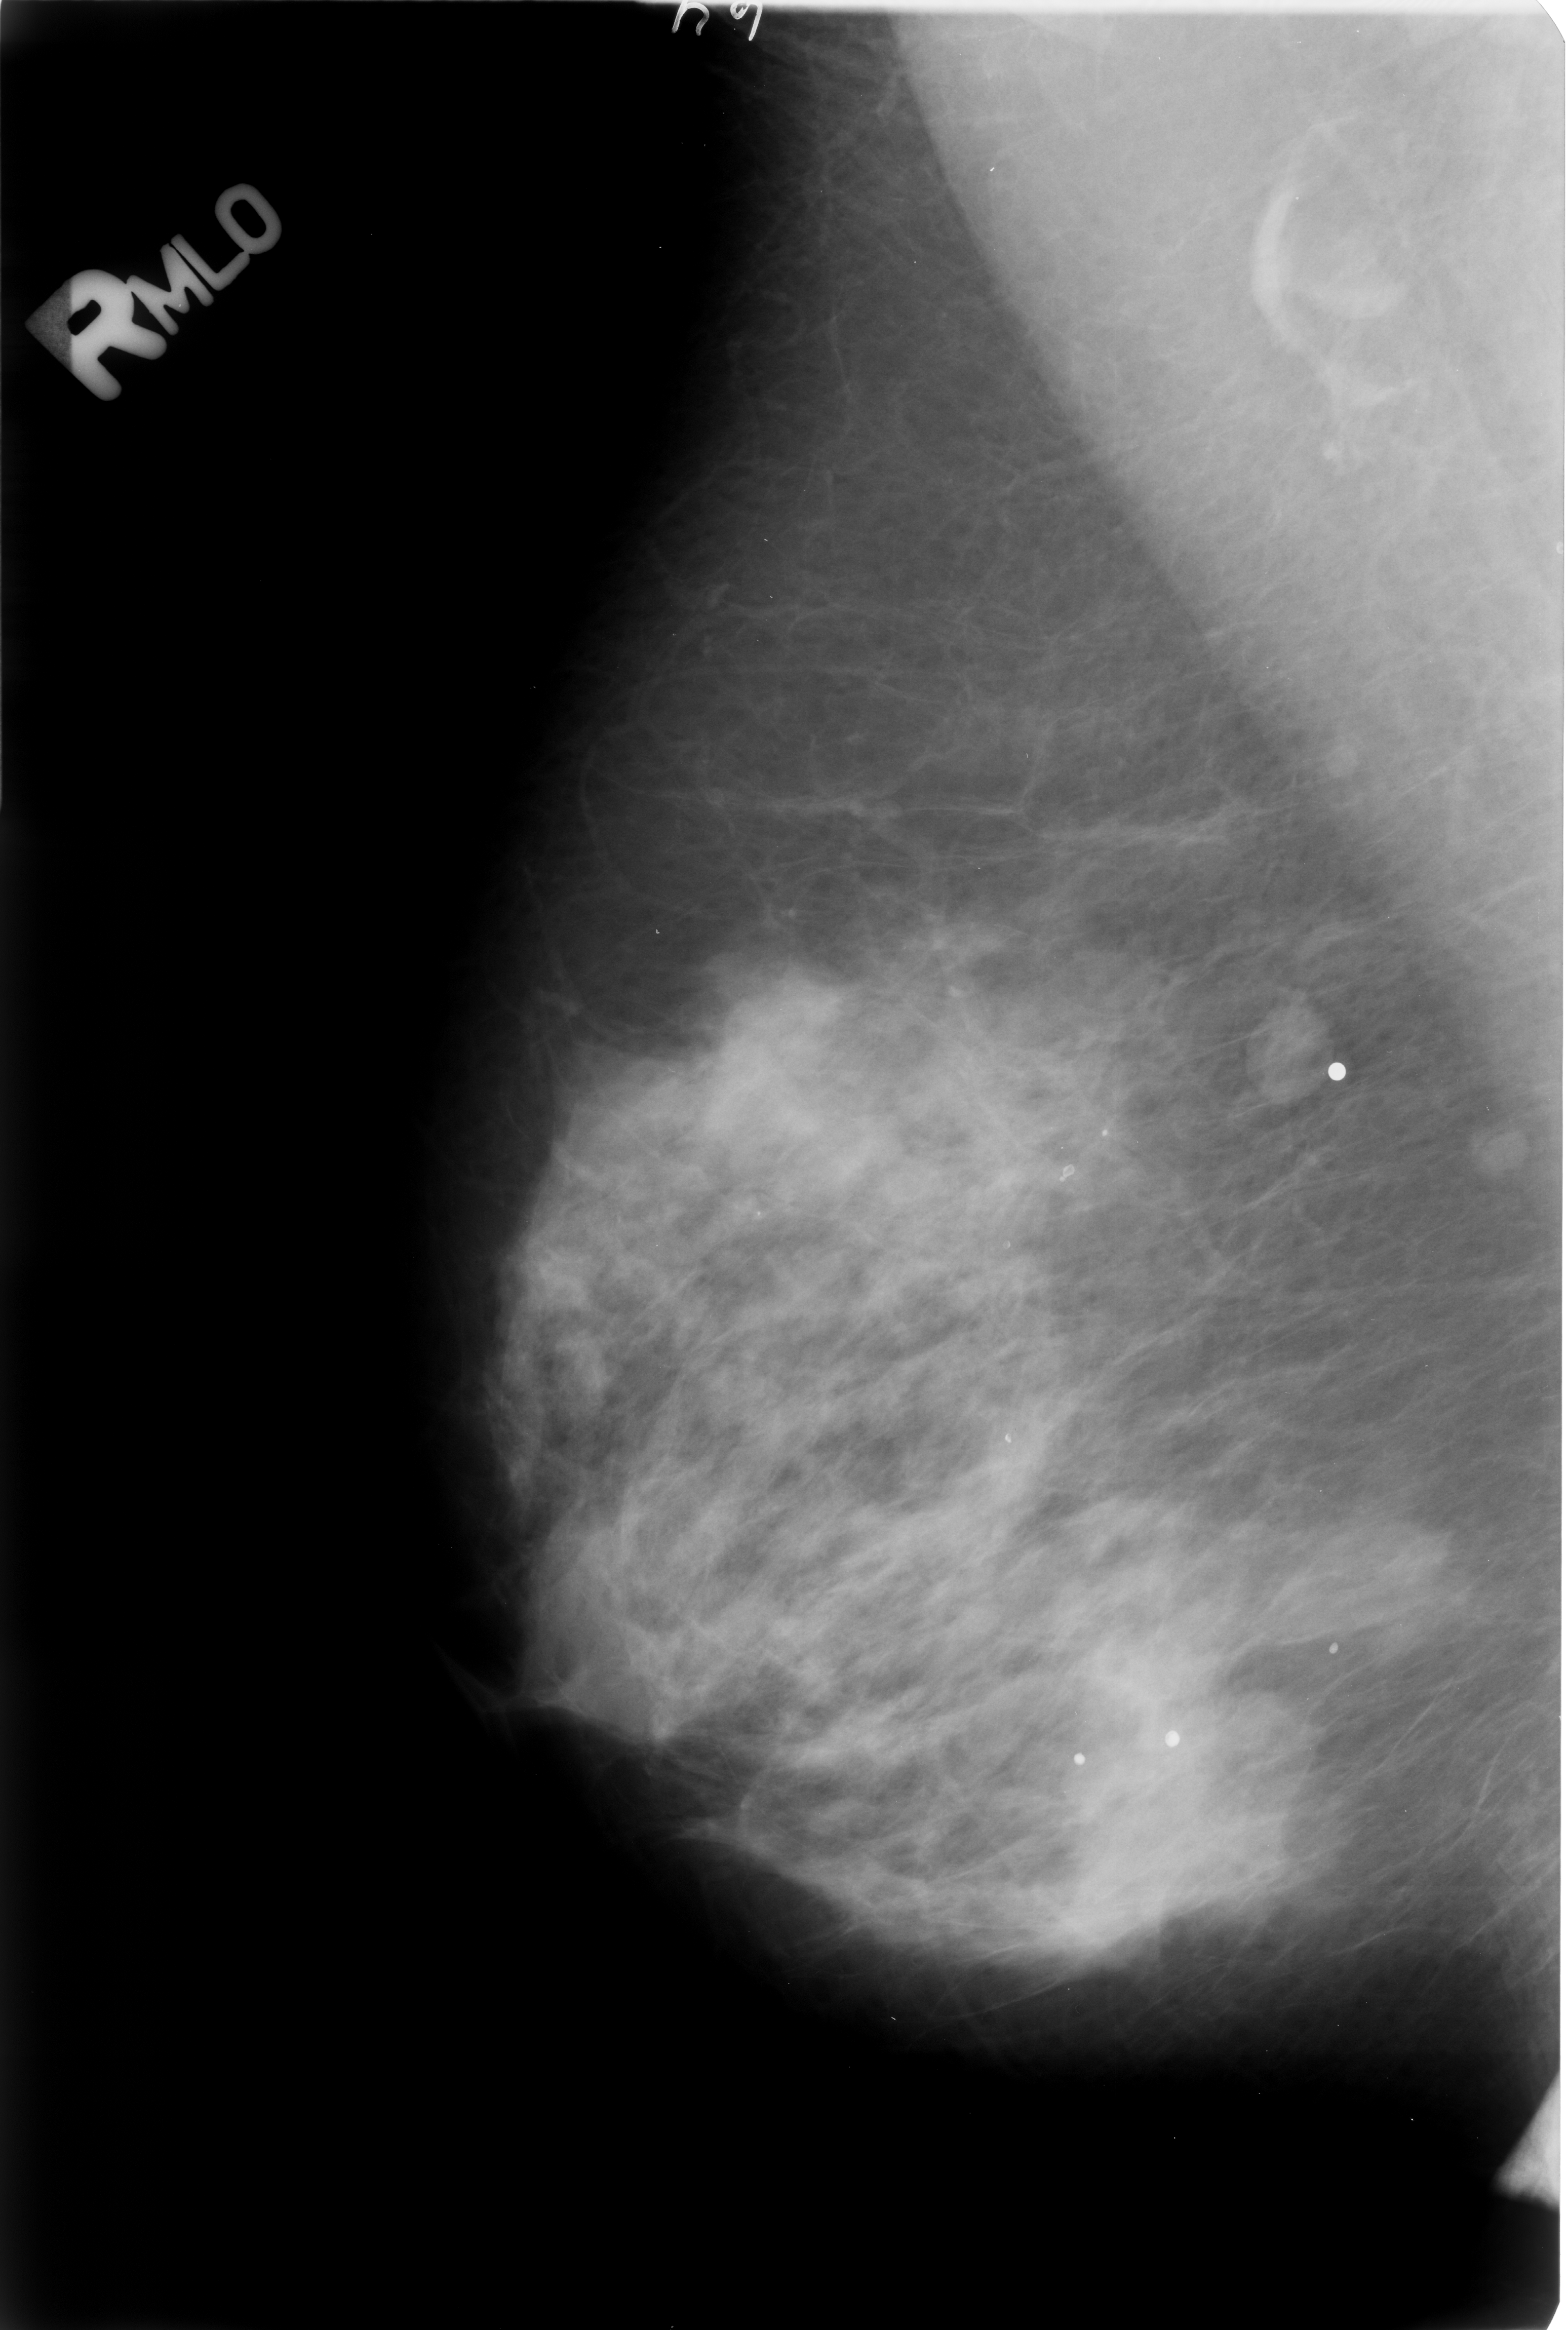
Mammogram (digitized film); right breast; MLO view; BI-RADS breast density category 3 (scale 1–4); 1568 × 2330 image matrix.
Marked abnormalities (boxes around the expert regions of interest):
- Finding 1 of 4: calcifications, morphology round and regular / lucent center; BI-RADS assessment category 2; outcome (as recorded, no biopsy): benign without callback (not worked up further): box from (x=1045, y=1150) to (x=1095, y=1209) px
- Finding 2 of 4: calcifications, morphology round and regular / lucent center; BI-RADS assessment category 2; subtlety rating 4 on a 1 (subtle) to 5 (obvious) scale; outcome (as recorded, no biopsy): benign without callback (not worked up further): (x=1061, y=1722)–(x=1107, y=1784)
- Finding 3 of 4: calcifications, morphology round and regular / lucent center; BI-RADS assessment category 2; outcome (as recorded, no biopsy): benign without callback (not worked up further): (x=1146, y=1718)–(x=1188, y=1768)
- Finding 4 of 4: calcifications, morphology round and regular / lucent center; BI-RADS assessment category 2; benign; no additional work-up was recommended (outcome (as recorded, no biopsy): benign without callback): (x=1304, y=1612)–(x=1383, y=1683)